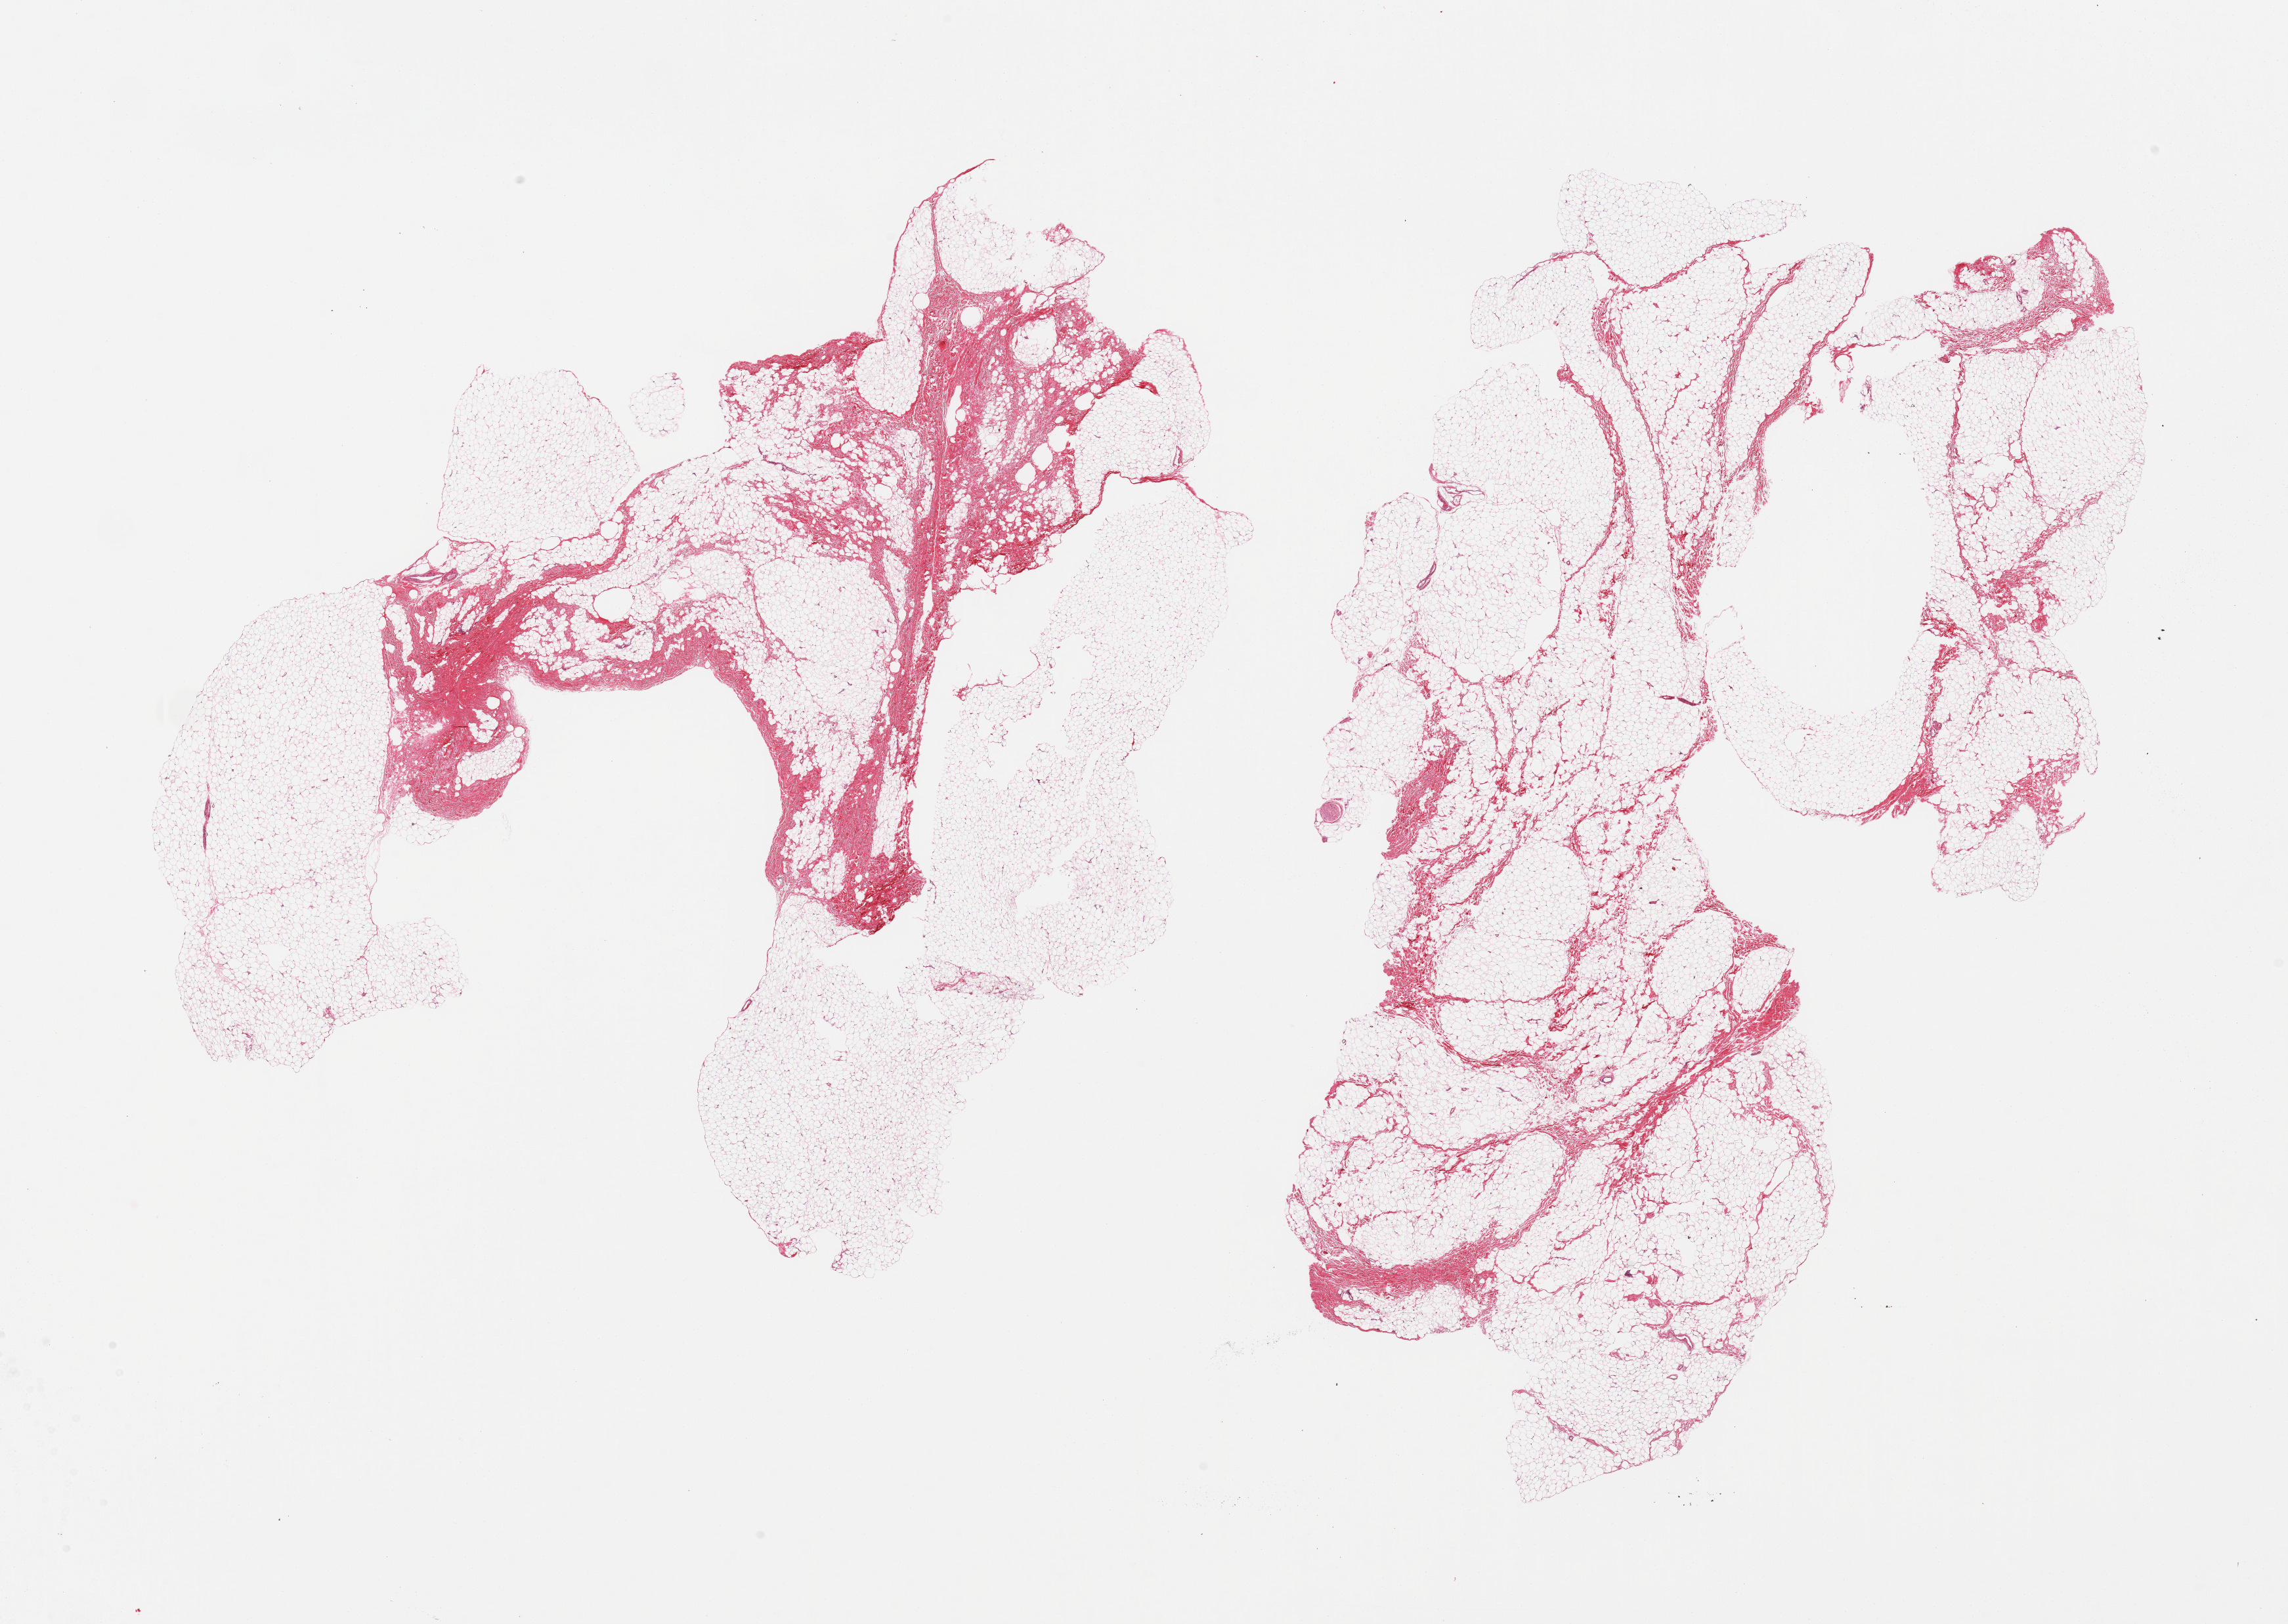
Digitized H&E-stained section — a low-resolution overview of the entire scanned area, about 27.6 x 19.6 mm. Donor: male.
• specimen: PAXgene-fixed paraffin-embedded (PFPE) section; section of breast (target tissue); tissue donor sample